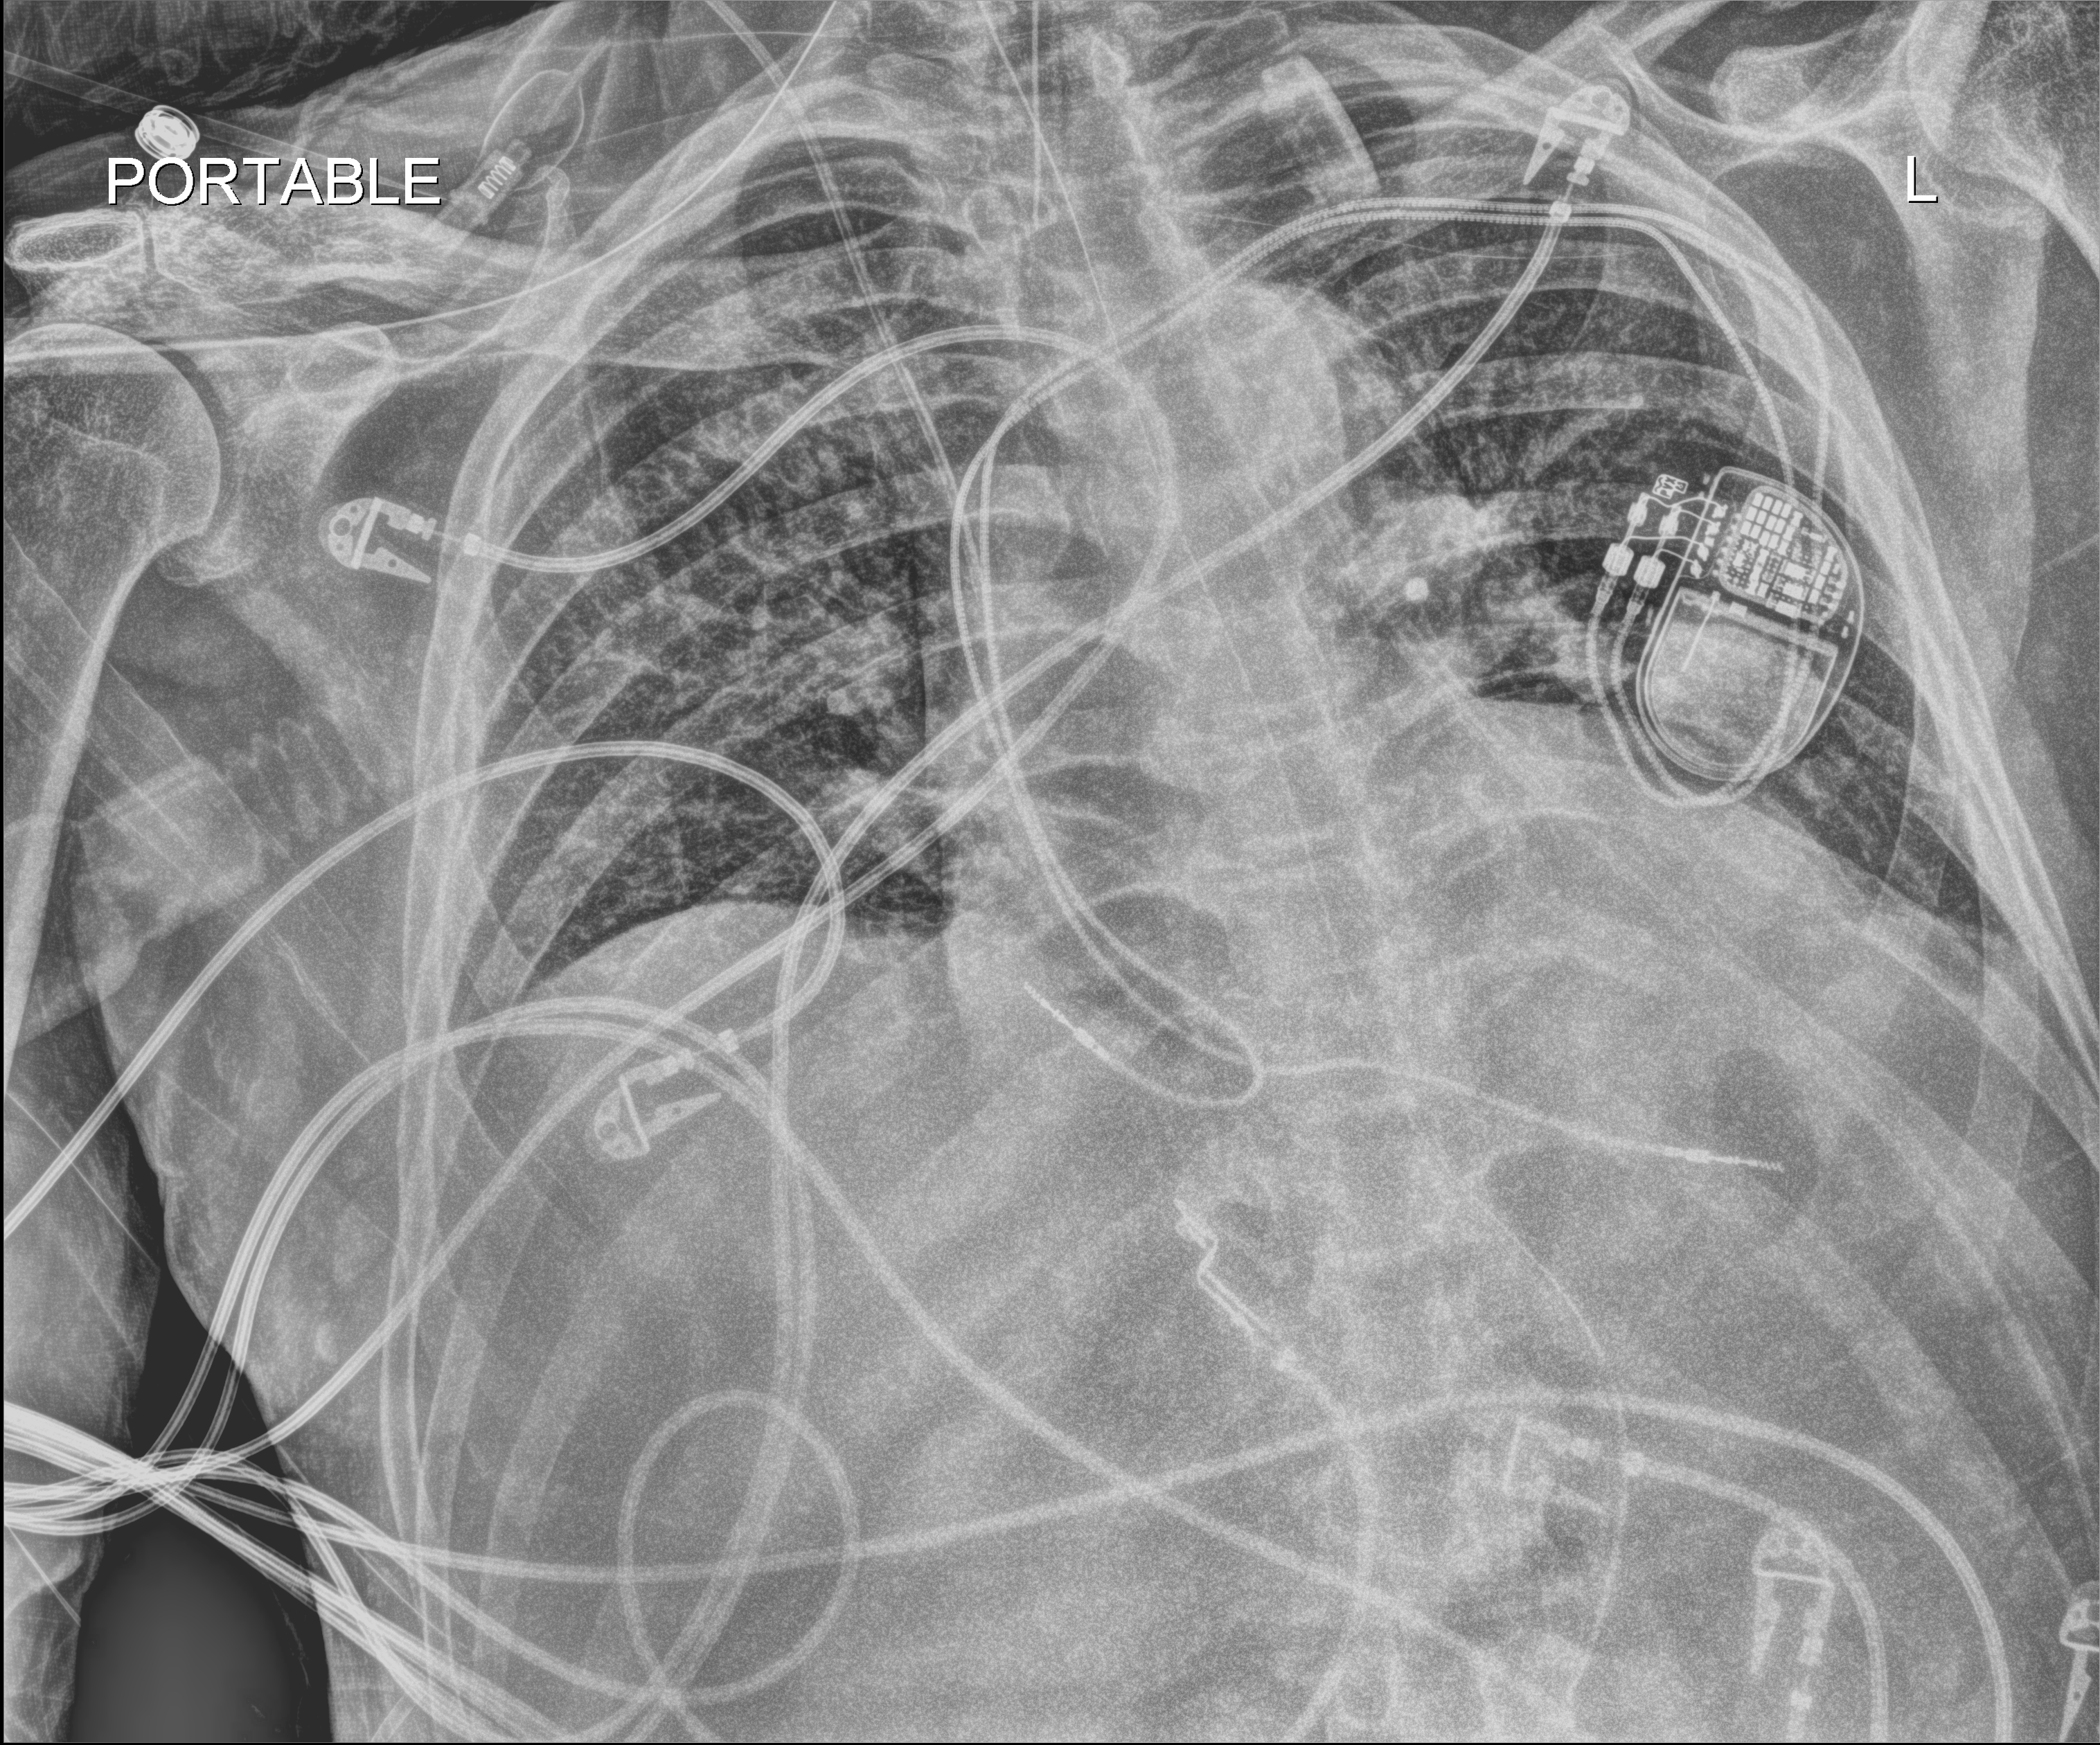
Portable chest radiograph. Male patient hospitalised with COVID-19, age 60–74 years.
Hospital-stay facts (about this admission, not read from this image; timing relative to this image not recorded): admitted to intensive care during this hospital stay: yes; mechanically ventilated during this hospital stay: yes.